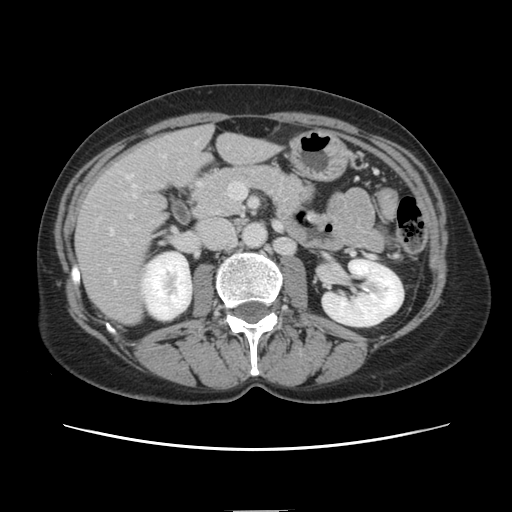
Contrast-enhanced abdominal CT, one axial slice. Slice 53 of 141 in the series (ordered by position). Intravenous contrast given. Soft-tissue window (W 400 / L 40 HU). 512 × 512 image matrix, field of view 350 × 350 mm. Female patient, age 63 years. Case-level facts recorded for this patient, not image findings: diagnosis: colorectal cancer liver metastases, imaged before liver resection; multiple liver metastases: yes; largest metastasis: 3.2 cm; chemotherapy before resection: yes.
Structures marked on this image (outlined manually by an expert reader):
- hepatic veins: bounding box <127,176,135,187> (left, top, right, bottom; pixels)
- liver: <76,127,276,325>
- planned liver remnant (the part of the liver to remain after resection): <178,128,276,178>
- portal vein (with intrahepatic branches): <111,174,133,234>